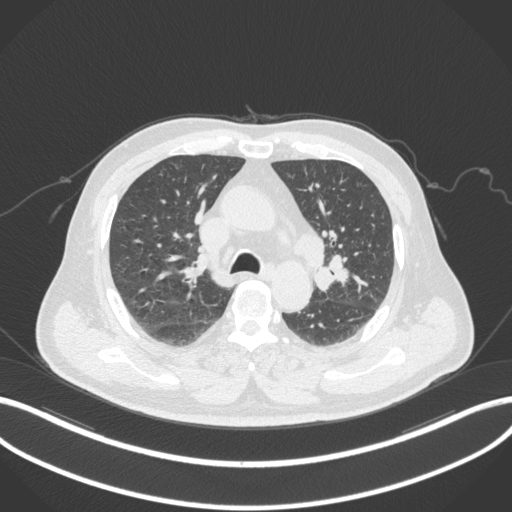
Chest CT, one axial slice; slice 198 of 286 in the series (ordered by position); lung window (W 1500 / L -600 HU); 1 mm slice thickness; 512 × 512 image matrix. Male patient, age 67 years. From the clinical record (not read from this slice): clinical TNM (as recorded): T2a N1 M0.
Outlined on this slice (rectangle marked by the reading radiologist):
- lung tumour (recorded histology: adenocarcinoma): box from (x=311, y=251) to (x=358, y=293) px